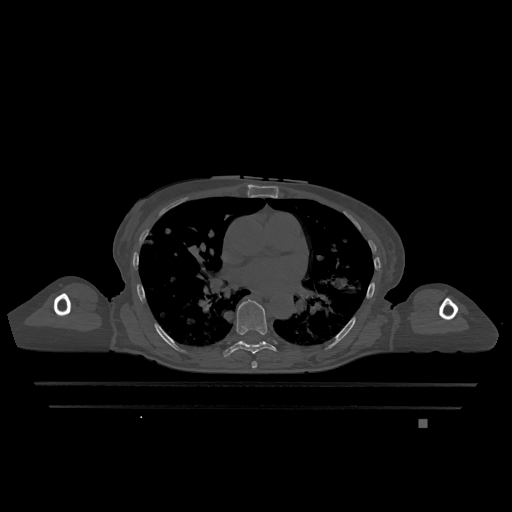
CT including the spine, one axial slice; slice 738 of 1317 in the series (ordered by position); bone window (W 1800 / L 400 HU); 0.5 mm slice thickness; 512 × 512 image matrix. Patient: female, 74 years. From the clinical record (not read from this slice): primary cancer: lung.
Annotated regions visible in this slice (semi-automatic segmentation, software-assisted and operator-edited):
- T6 vertebra: bounding box [x1, y1, x2, y2] px = [252, 361, 258, 368]
- T7 vertebra: [223, 300, 277, 357]